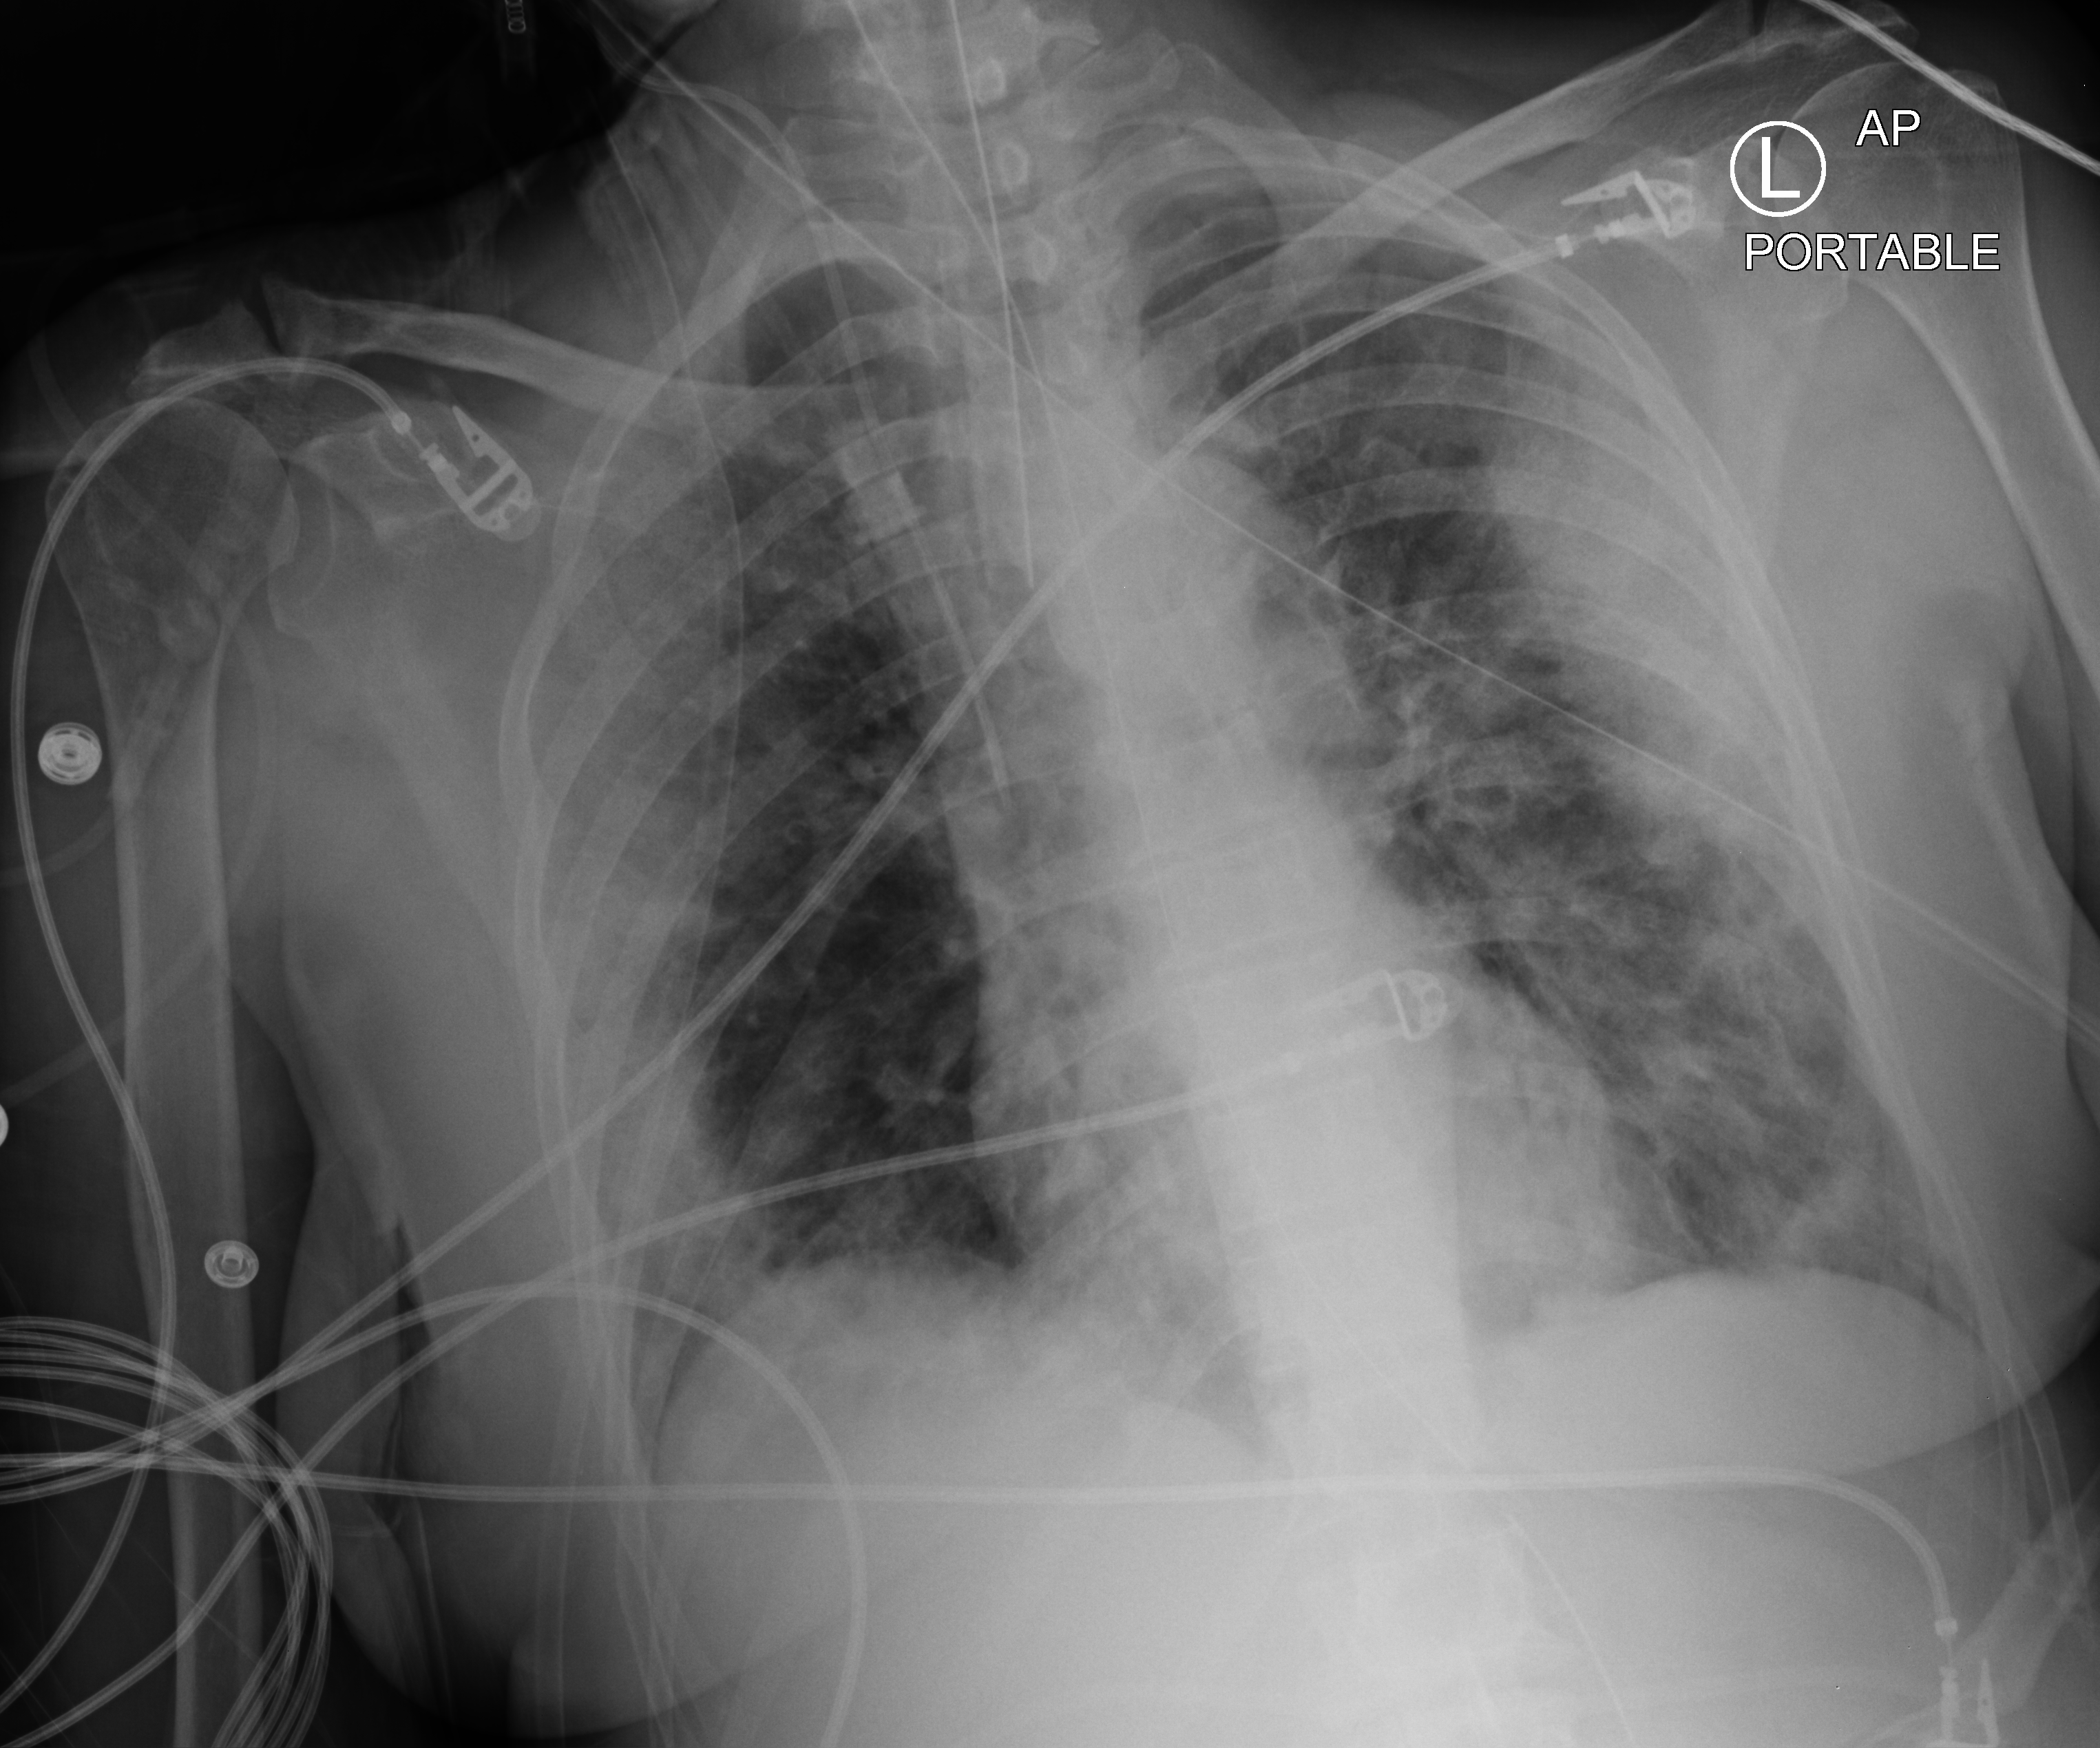
Bedside chest radiograph (computed radiography); anteroposterior (AP) projection. Female patient hospitalised with COVID-19, age 60–74 years.
Hospital-stay facts (about this admission, not read from this image; timing relative to this image not recorded):
- other chronic lung disease (admission record): no
- smoking status (admission record): former